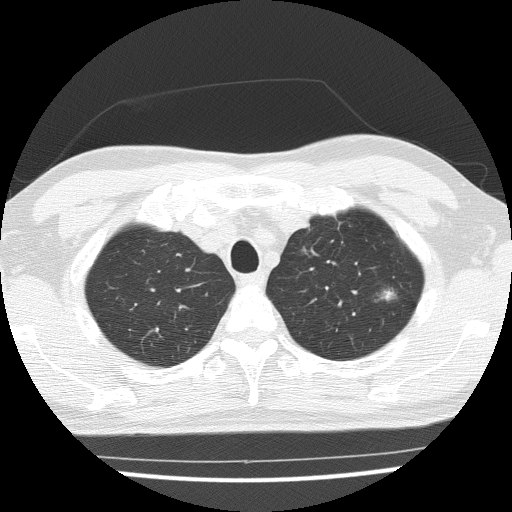
Chest CT (low-dose screening protocol), one axial image. Third annual screen. Lung window (W 1500 / L -600 HU). 2 mm slice thickness. Lung (sharp) reconstruction kernel (FC51). 120 kVp. 512 × 512 image matrix, field of view 330 × 330 mm. Male, age 65 years at enrolment. Current smoker at enrolment.
• Expert-annotated lung lesion, bounding box (x1, y1, x2, y2) in pixels: (359, 274, 414, 322).
• Reader record for this screening exam (exam-level; its link to the box is not recorded): non-calcified nodule or mass ≥4 mm, left upper lobe, 16 × 15 mm, poorly defined margins, soft tissue attenuation, pre-existing on the prior screen: yes; interval growth: yes.
• Lung cancer was diagnosed 42 days after this screen: squamous cell carcinoma, NOS, left upper lobe, moderately differentiated (G2), stage IA (AJCC 6th edition), 25 mm at pathology.